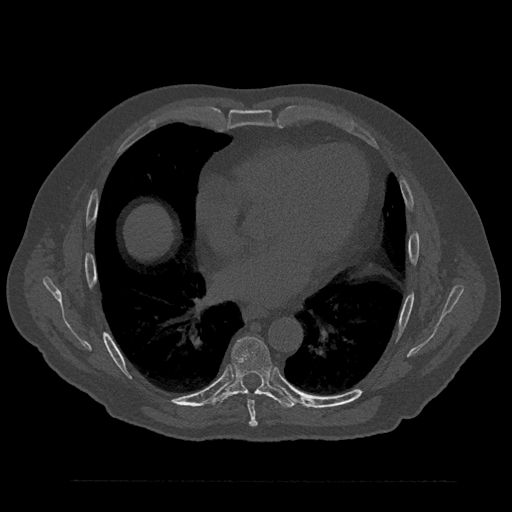
CT including the spine, one axial slice; position 473 of 797 along the scan axis; reconstruction kernel Br40s/3; 120 kVp; bone window (W 1800 / L 400 HU); 0.5 mm slice thickness; 512 × 512 image matrix. Patient: male, 61 years. From the clinical record (not read from this slice): primary cancer: prostate.
Outlined on this slice (semi-automatic segmentation, software-assisted and operator-edited):
- T7 vertebra: bounding box <242,391,258,427> (left, top, right, bottom; pixels)
- T8 vertebra: <211,336,296,408>